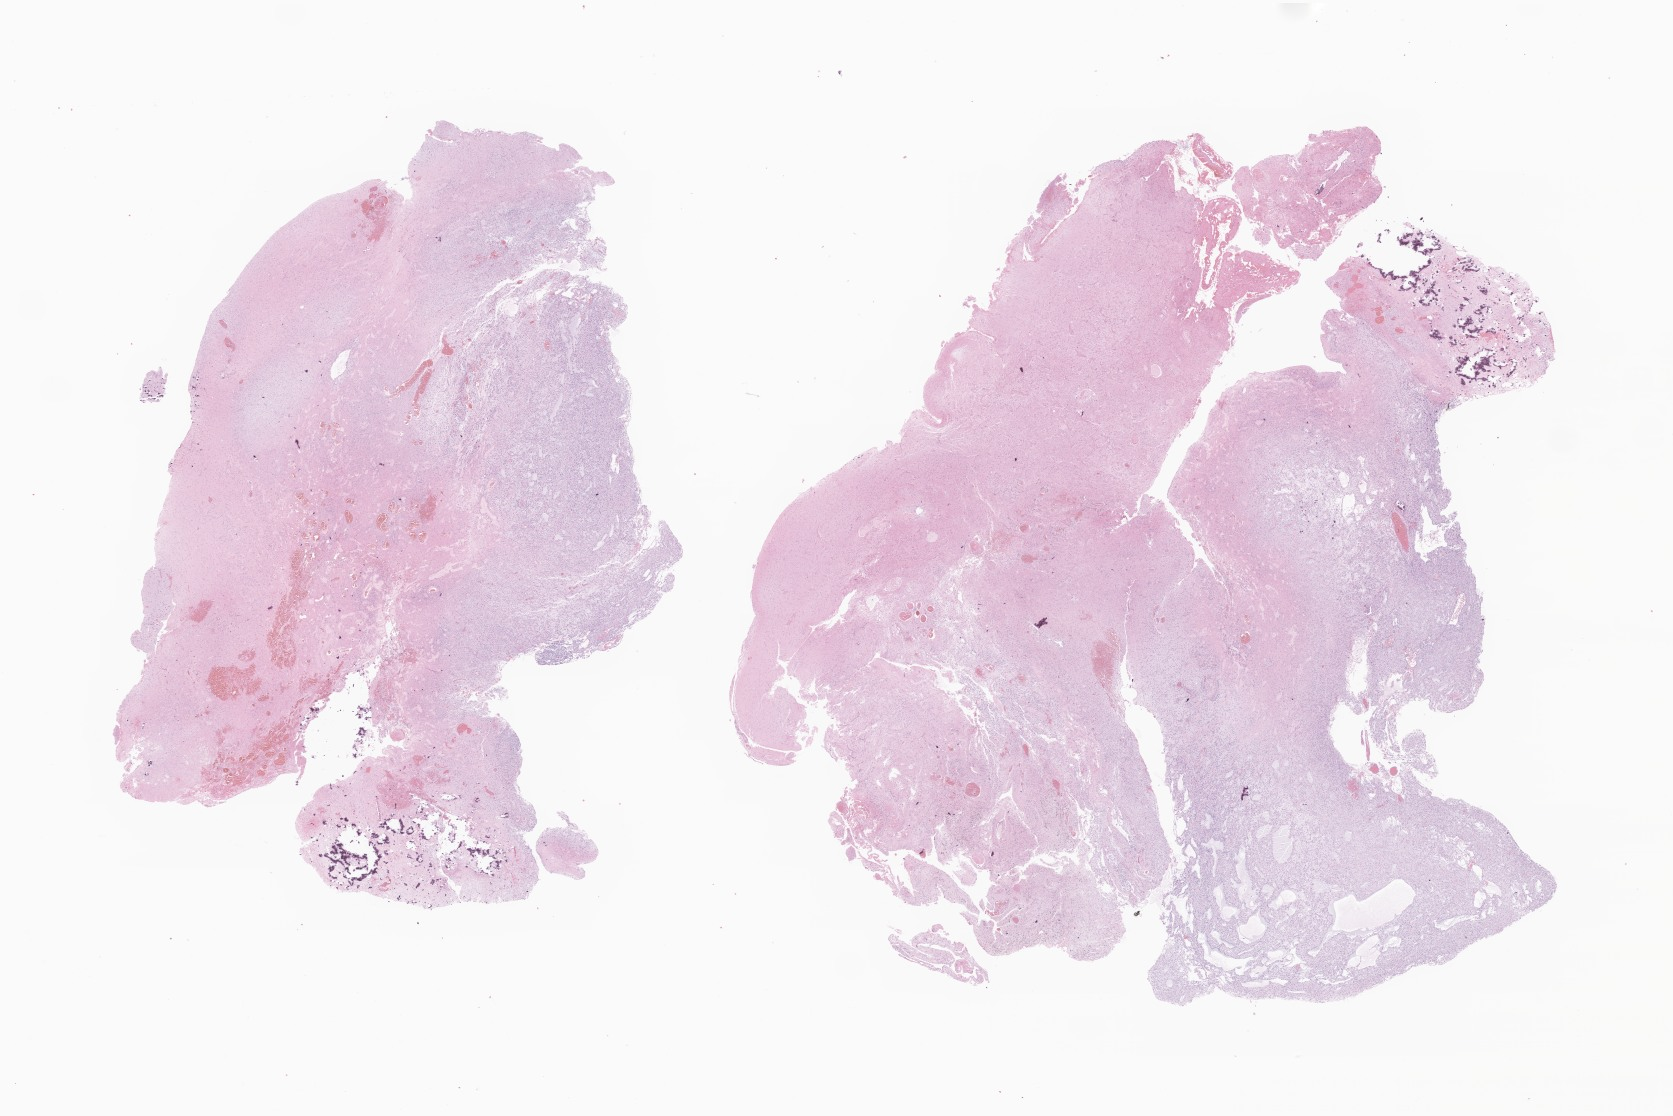
Digitized H&E-stained section of tumor tissue from the brain, low-resolution overview of the scanned area, about 28.2 x 18.8 mm, formalin-fixed, paraffin-embedded (FFPE) tissue. Patient male; age 199 months (16 years 7 months).
- diagnosis (ICD-O-3 morphology term): Neoplasm, uncertain whether benign or malignant